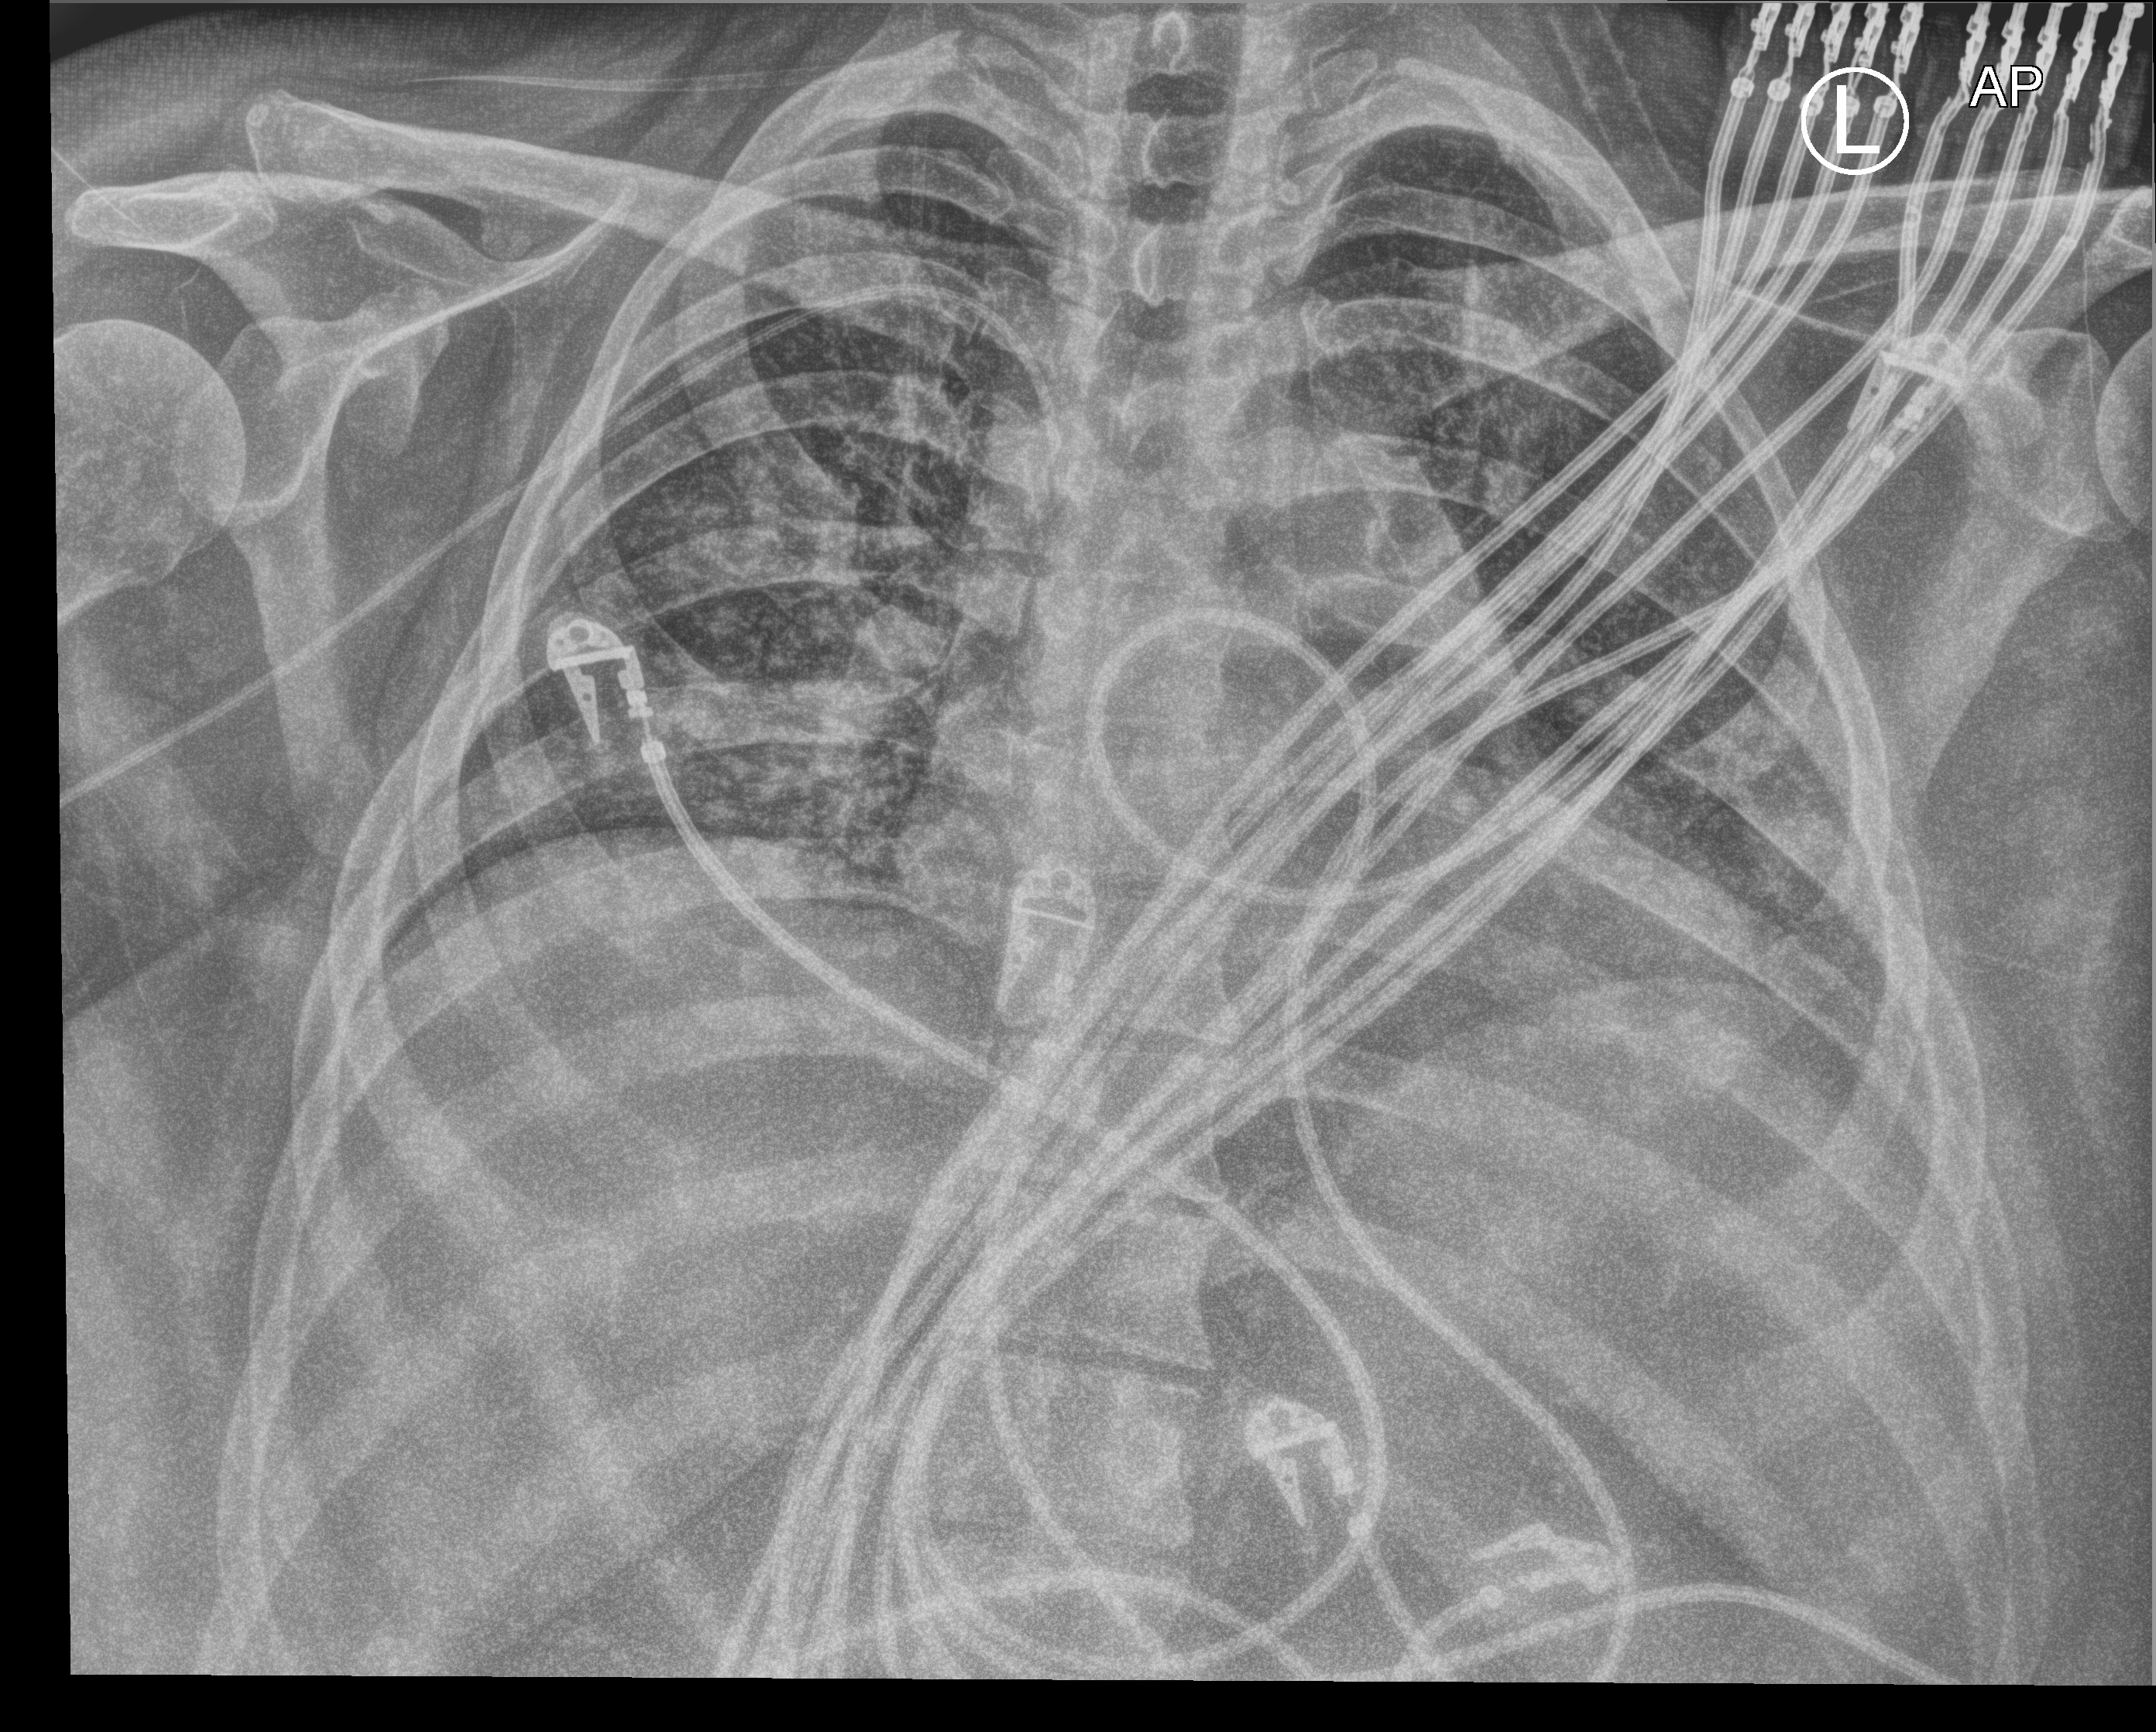
Portable chest radiograph, anteroposterior (AP) projection. Patient hospitalised with COVID-19; female, aged 18–59 years.
Admission-level facts for this patient (not findings on this image; timing relative to this image not recorded): mechanically ventilated during this hospital stay: yes.